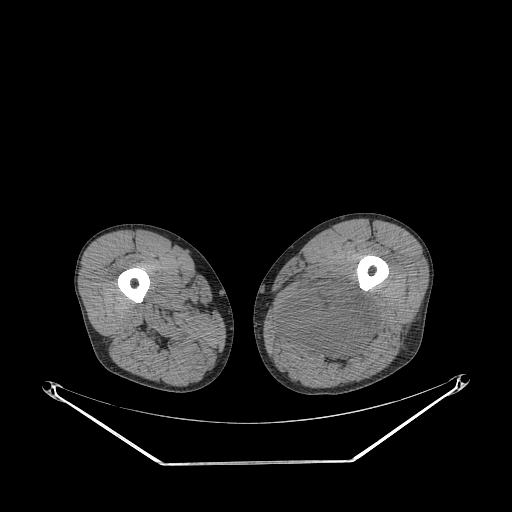
CT of an extremity soft-tissue mass (from a PET/CT study), one axial slice; slice 241 of 267 in the series (ordered by position); reconstruction kernel STANDARD; 140 kVp; soft-tissue window (W 400 / L 40 HU); 512 × 512 image matrix. Male patient. Case-level facts recorded for this patient, not image findings: histological type: undifferentiated pleomorphic liposarcoma; grade: high; site of the primary tumour: left thigh.
Structures marked on this image (expert contour drawn on MRI and transferred to this co-registered scan by the dataset authors):
- gross tumour volume including surrounding oedema: bounding box <278,283,376,362> (left, top, right, bottom; pixels)
- gross tumour volume (mass): <279,283,376,355>